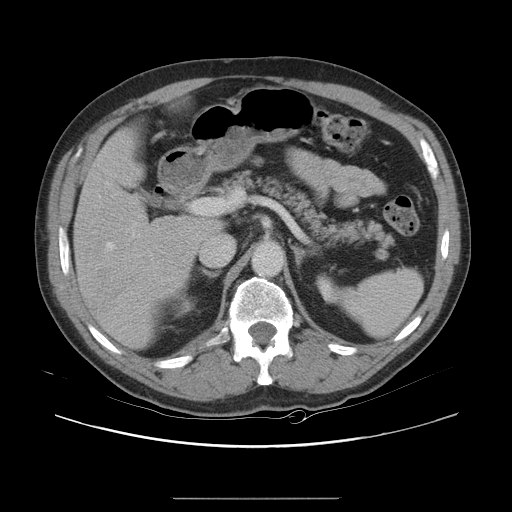
Contrast-enhanced abdominal CT, one axial slice; slice 13 of 40 in the series (ordered by position); 120 kVp; soft-tissue window (W 400 / L 40 HU); 5 mm slice thickness; 512 × 512 image matrix, field of view 408 × 408 mm. Male patient, age 64 years. From the clinical record (not read from this slice): diagnosis: colorectal cancer liver metastases, imaged before liver resection; multiple liver metastases: yes; largest metastasis: 3.2 cm; chemotherapy before resection: yes.
Structures marked on this image (expert manual segmentation):
- hepatic veins: bounding box [x1, y1, x2, y2] px = [107, 242, 114, 249]
- liver: [75, 131, 218, 347]
- planned liver remnant (the part of the liver to remain after resection): [88, 131, 218, 238]